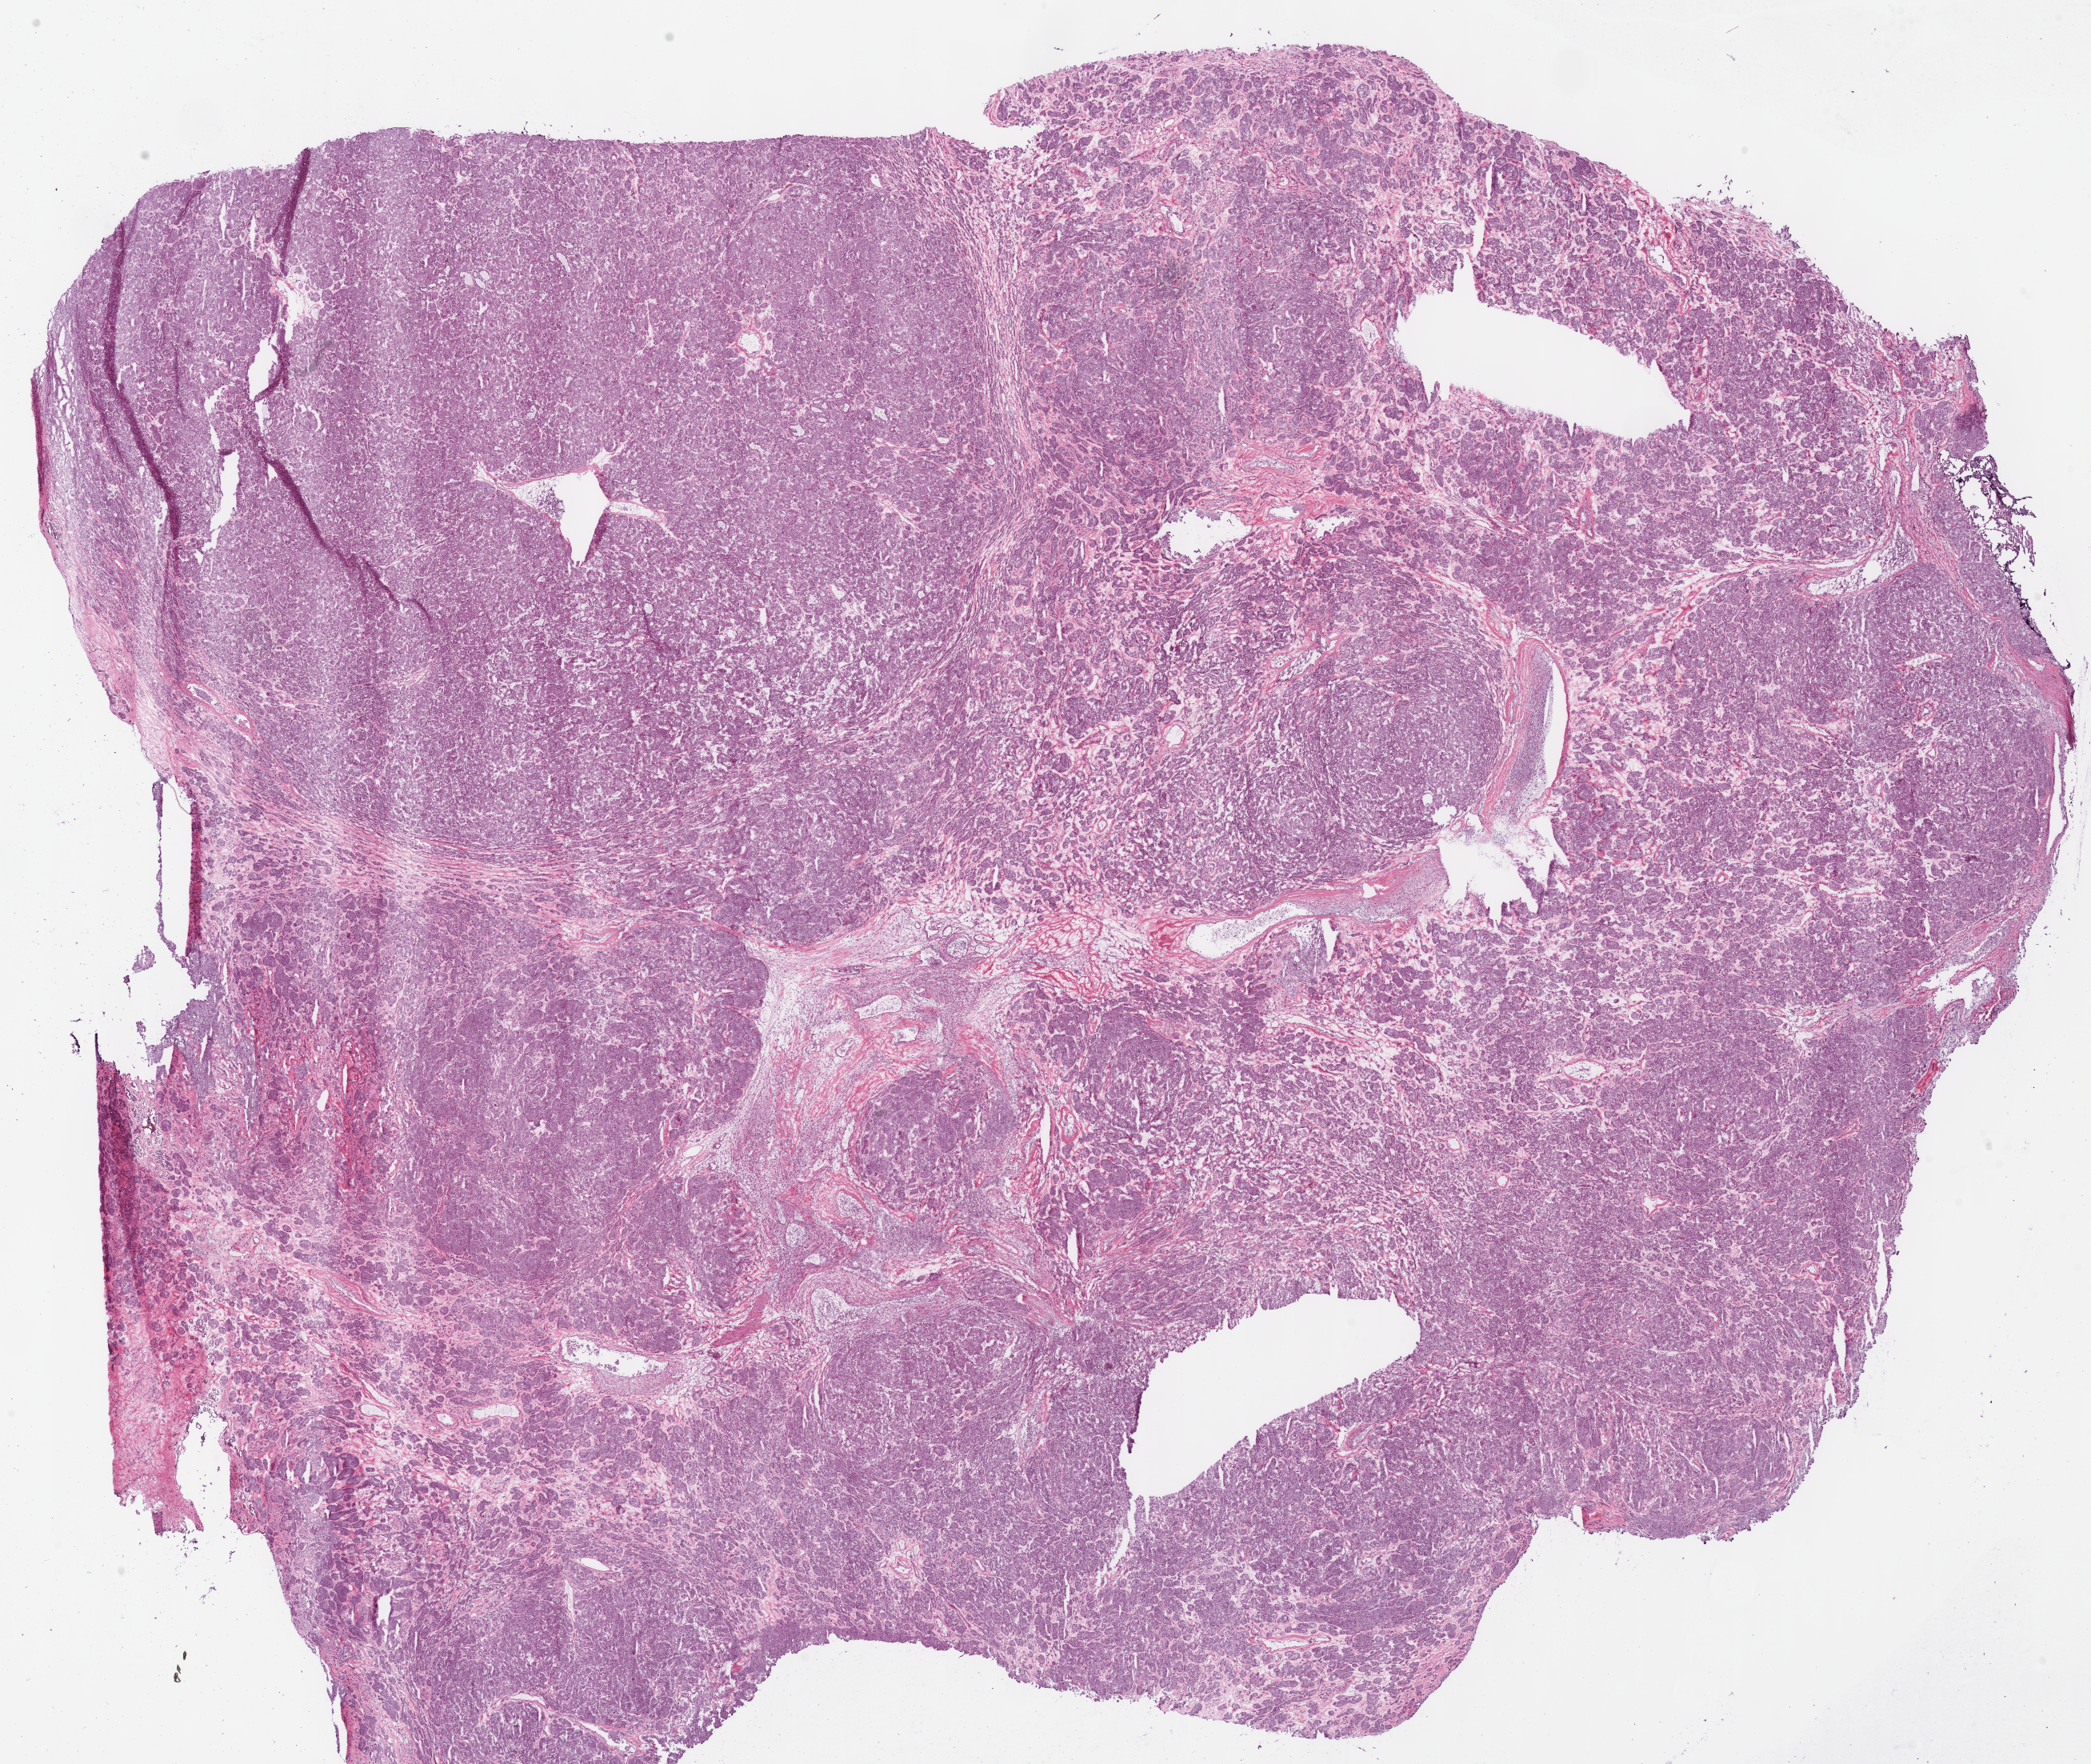
Digitized H&E-stained tissue section (whole slide) — low-resolution overview of the scanned area, about 20.6 x 17.3 mm, frozen section, kidney, primary tumour sample. Male patient; age at initial diagnosis 51 years.
Pathologic diagnosis: Renal cell carcinoma, chromophobe type.